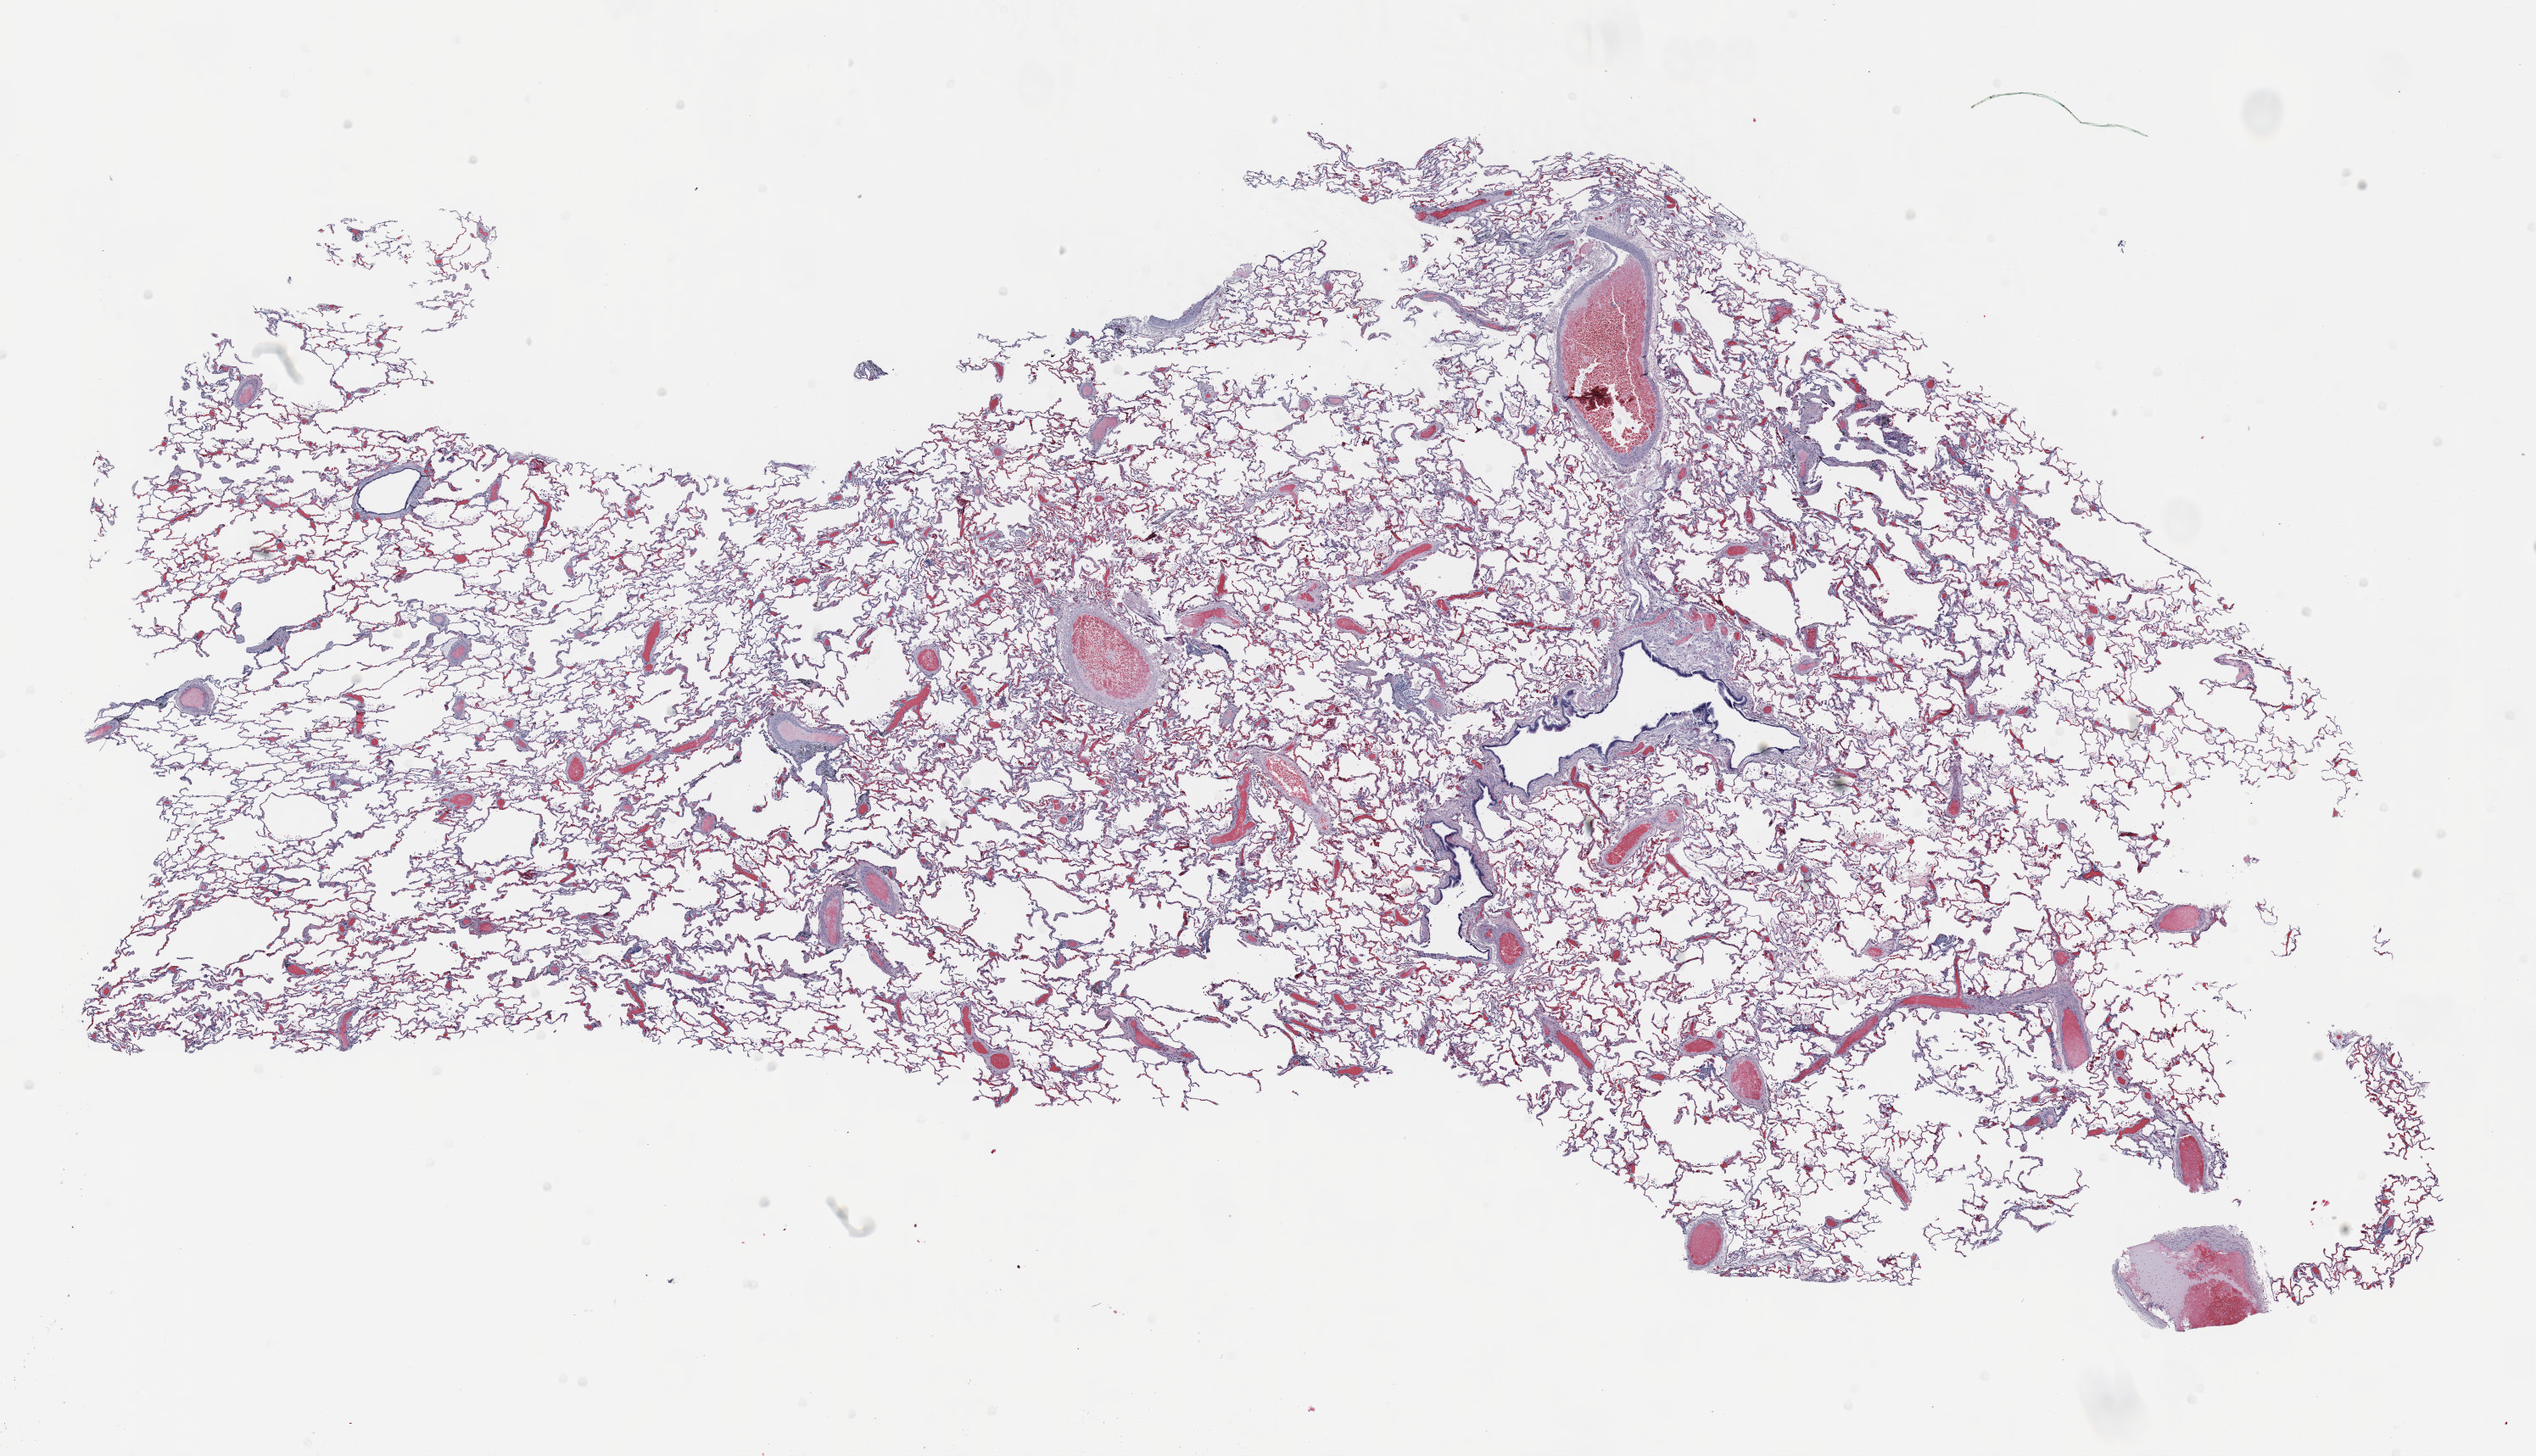
H&E-stained whole-slide image, low-resolution overview of the scanned area, about 24.0 x 13.8 mm (from a 20x scan); formalin-fixed paraffin-embedded (FFPE) section; lung tissue. Male, age 56 at enrolment. Former smoker at enrolment.
Participant's lung-cancer diagnosis: Adenocarcinoma, NOS (ICD-O-3 8140/3).